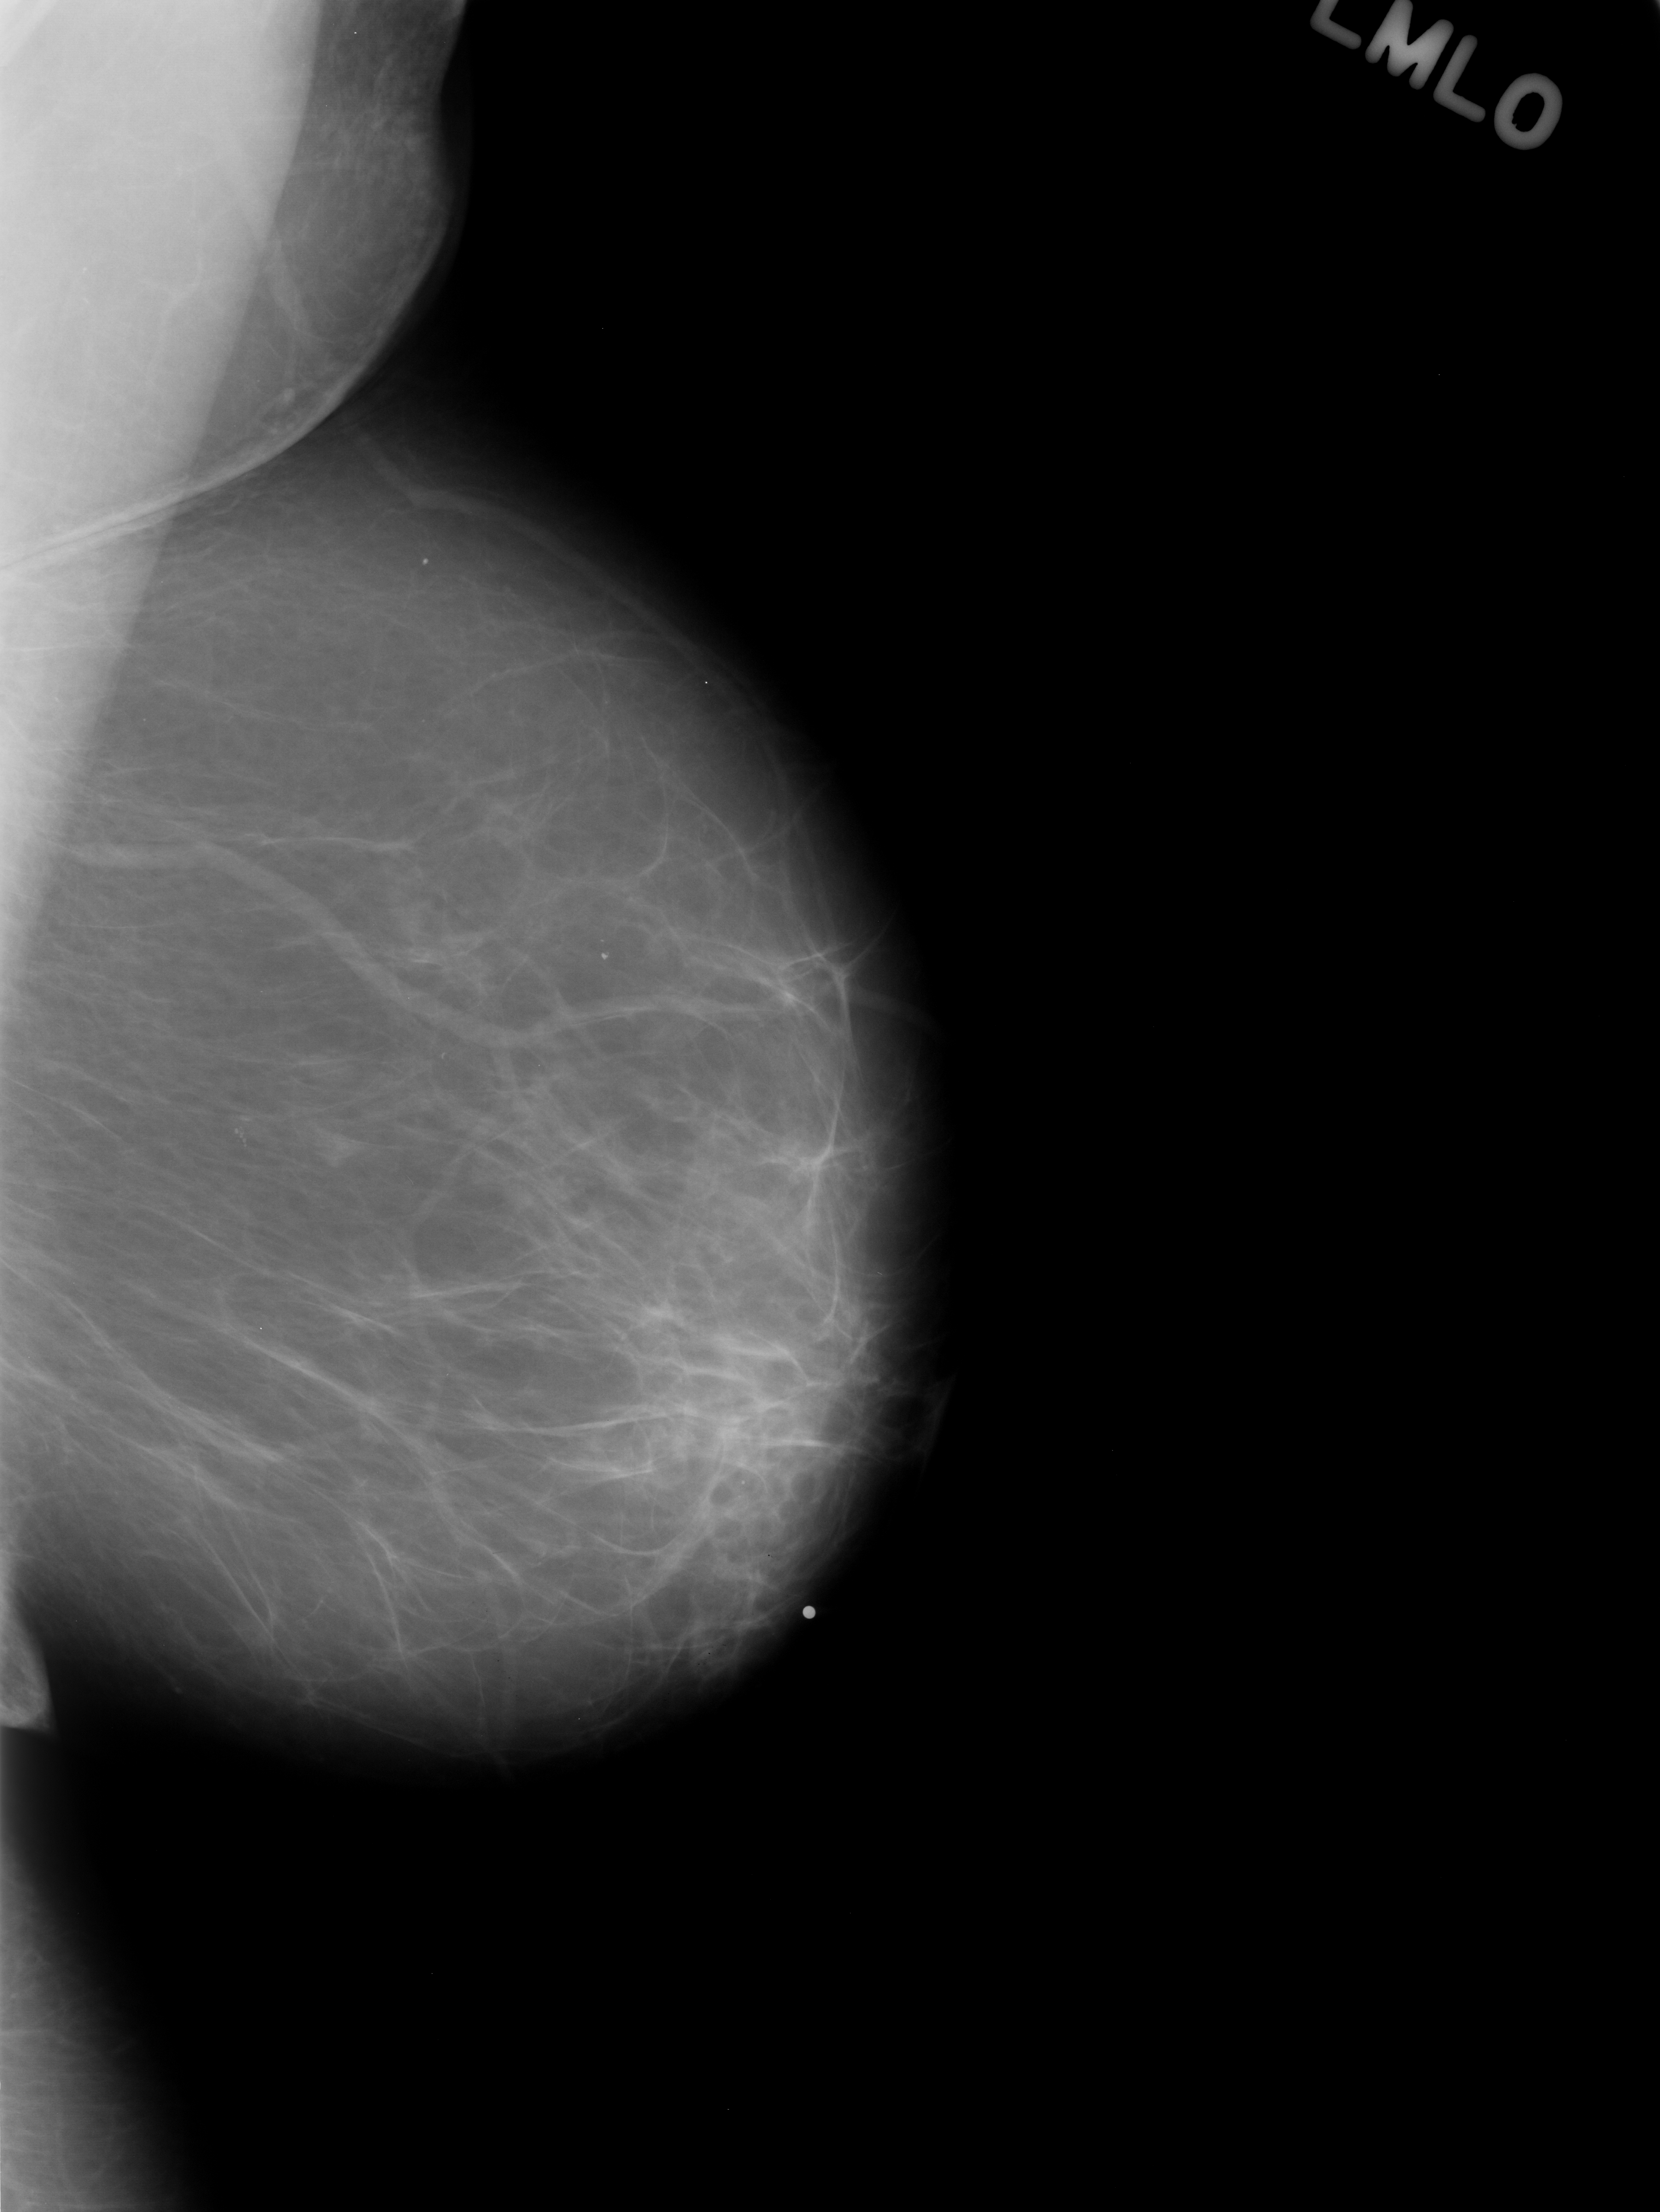
Scanned film-screen mammogram; left breast; mediolateral oblique (MLO) view; 1660 × 2212 image matrix.
Expert-marked regions of interest on this film, with their recorded descriptors:
- mass, shape focal asymmetric density, margins ill defined; BI-RADS assessment category 3; subtlety rating 5 on a 1 (subtle) to 5 (obvious) scale; pathology (as recorded): benign: bounding box (x1, y1, x2, y2) in pixels: (700, 1456, 848, 1638)